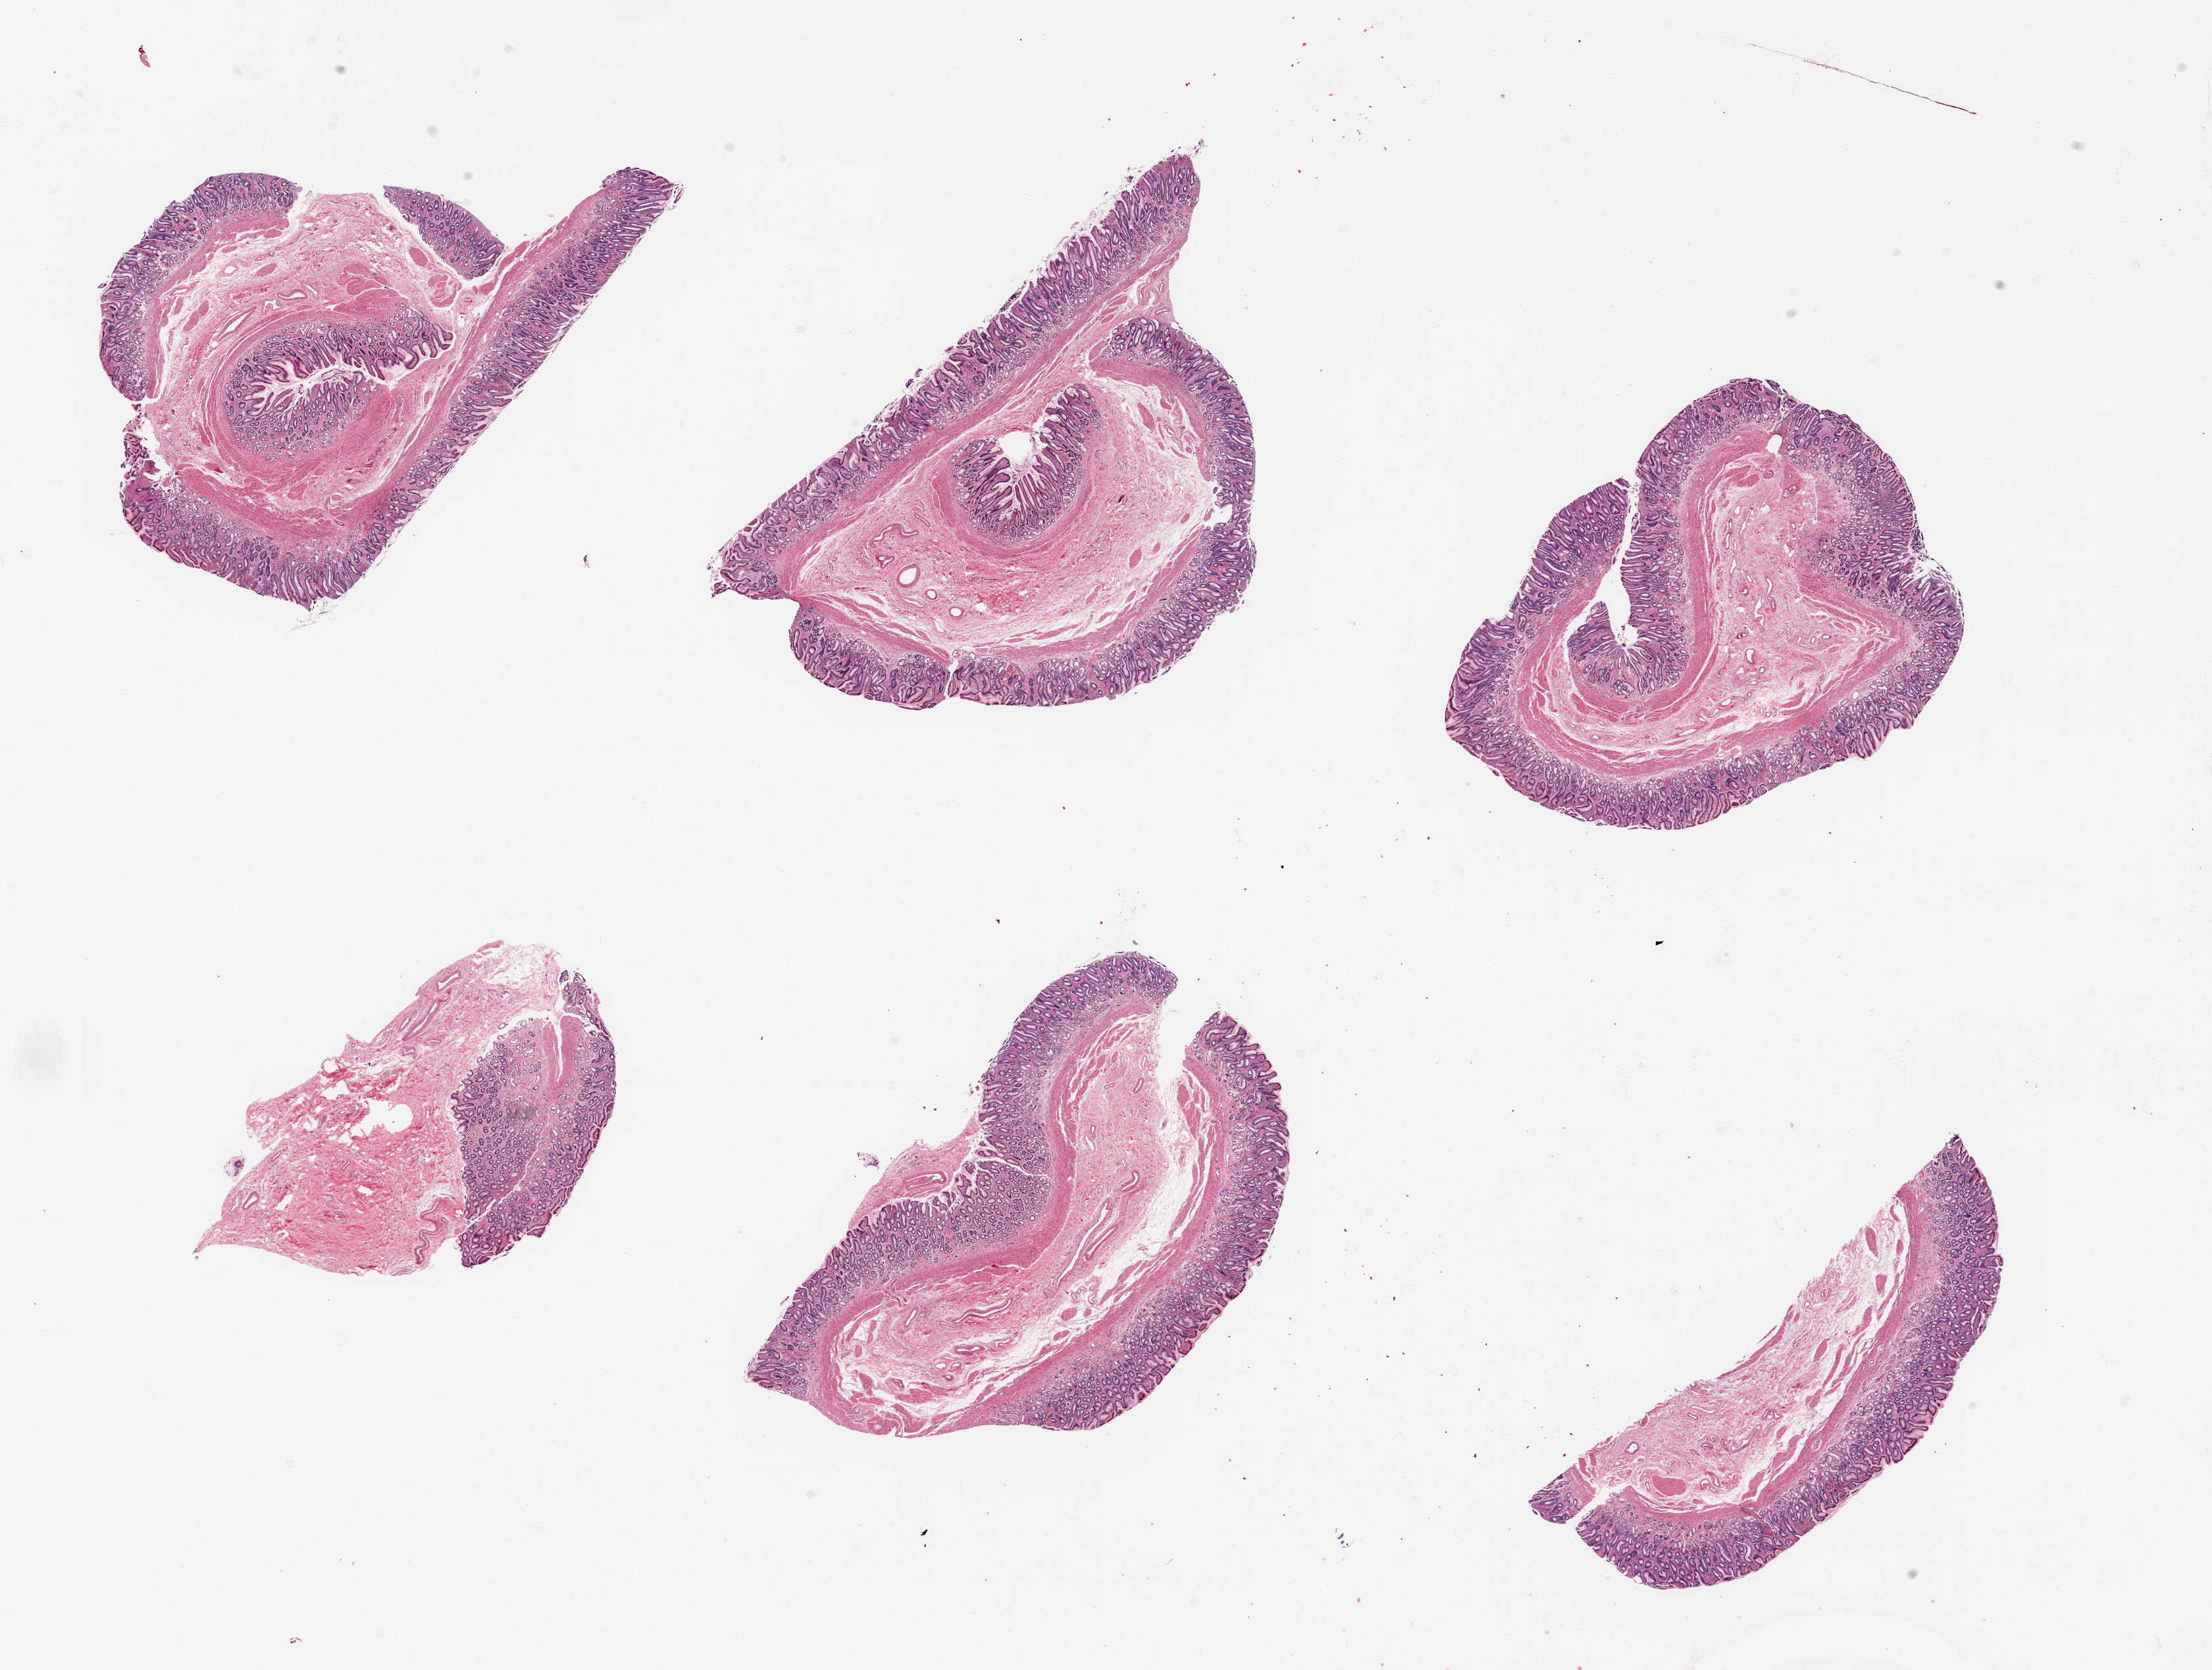
Whole-slide image, hematoxylin and eosin (H&E) stain, shown as a low-resolution overview of the whole scanned area (about 26.6 x 20.1 mm), PAXgene-fixed, paraffin-embedded tissue, target tissue: stomach, donor tissue sample. Donor sex: female.
* reviewer comment on this tissue sample: 6 pieces, well preserved mucosa, ~0.5-0.8mm thick, 30-50% thickness, mainly antral with prominent foveolargastropathic changes